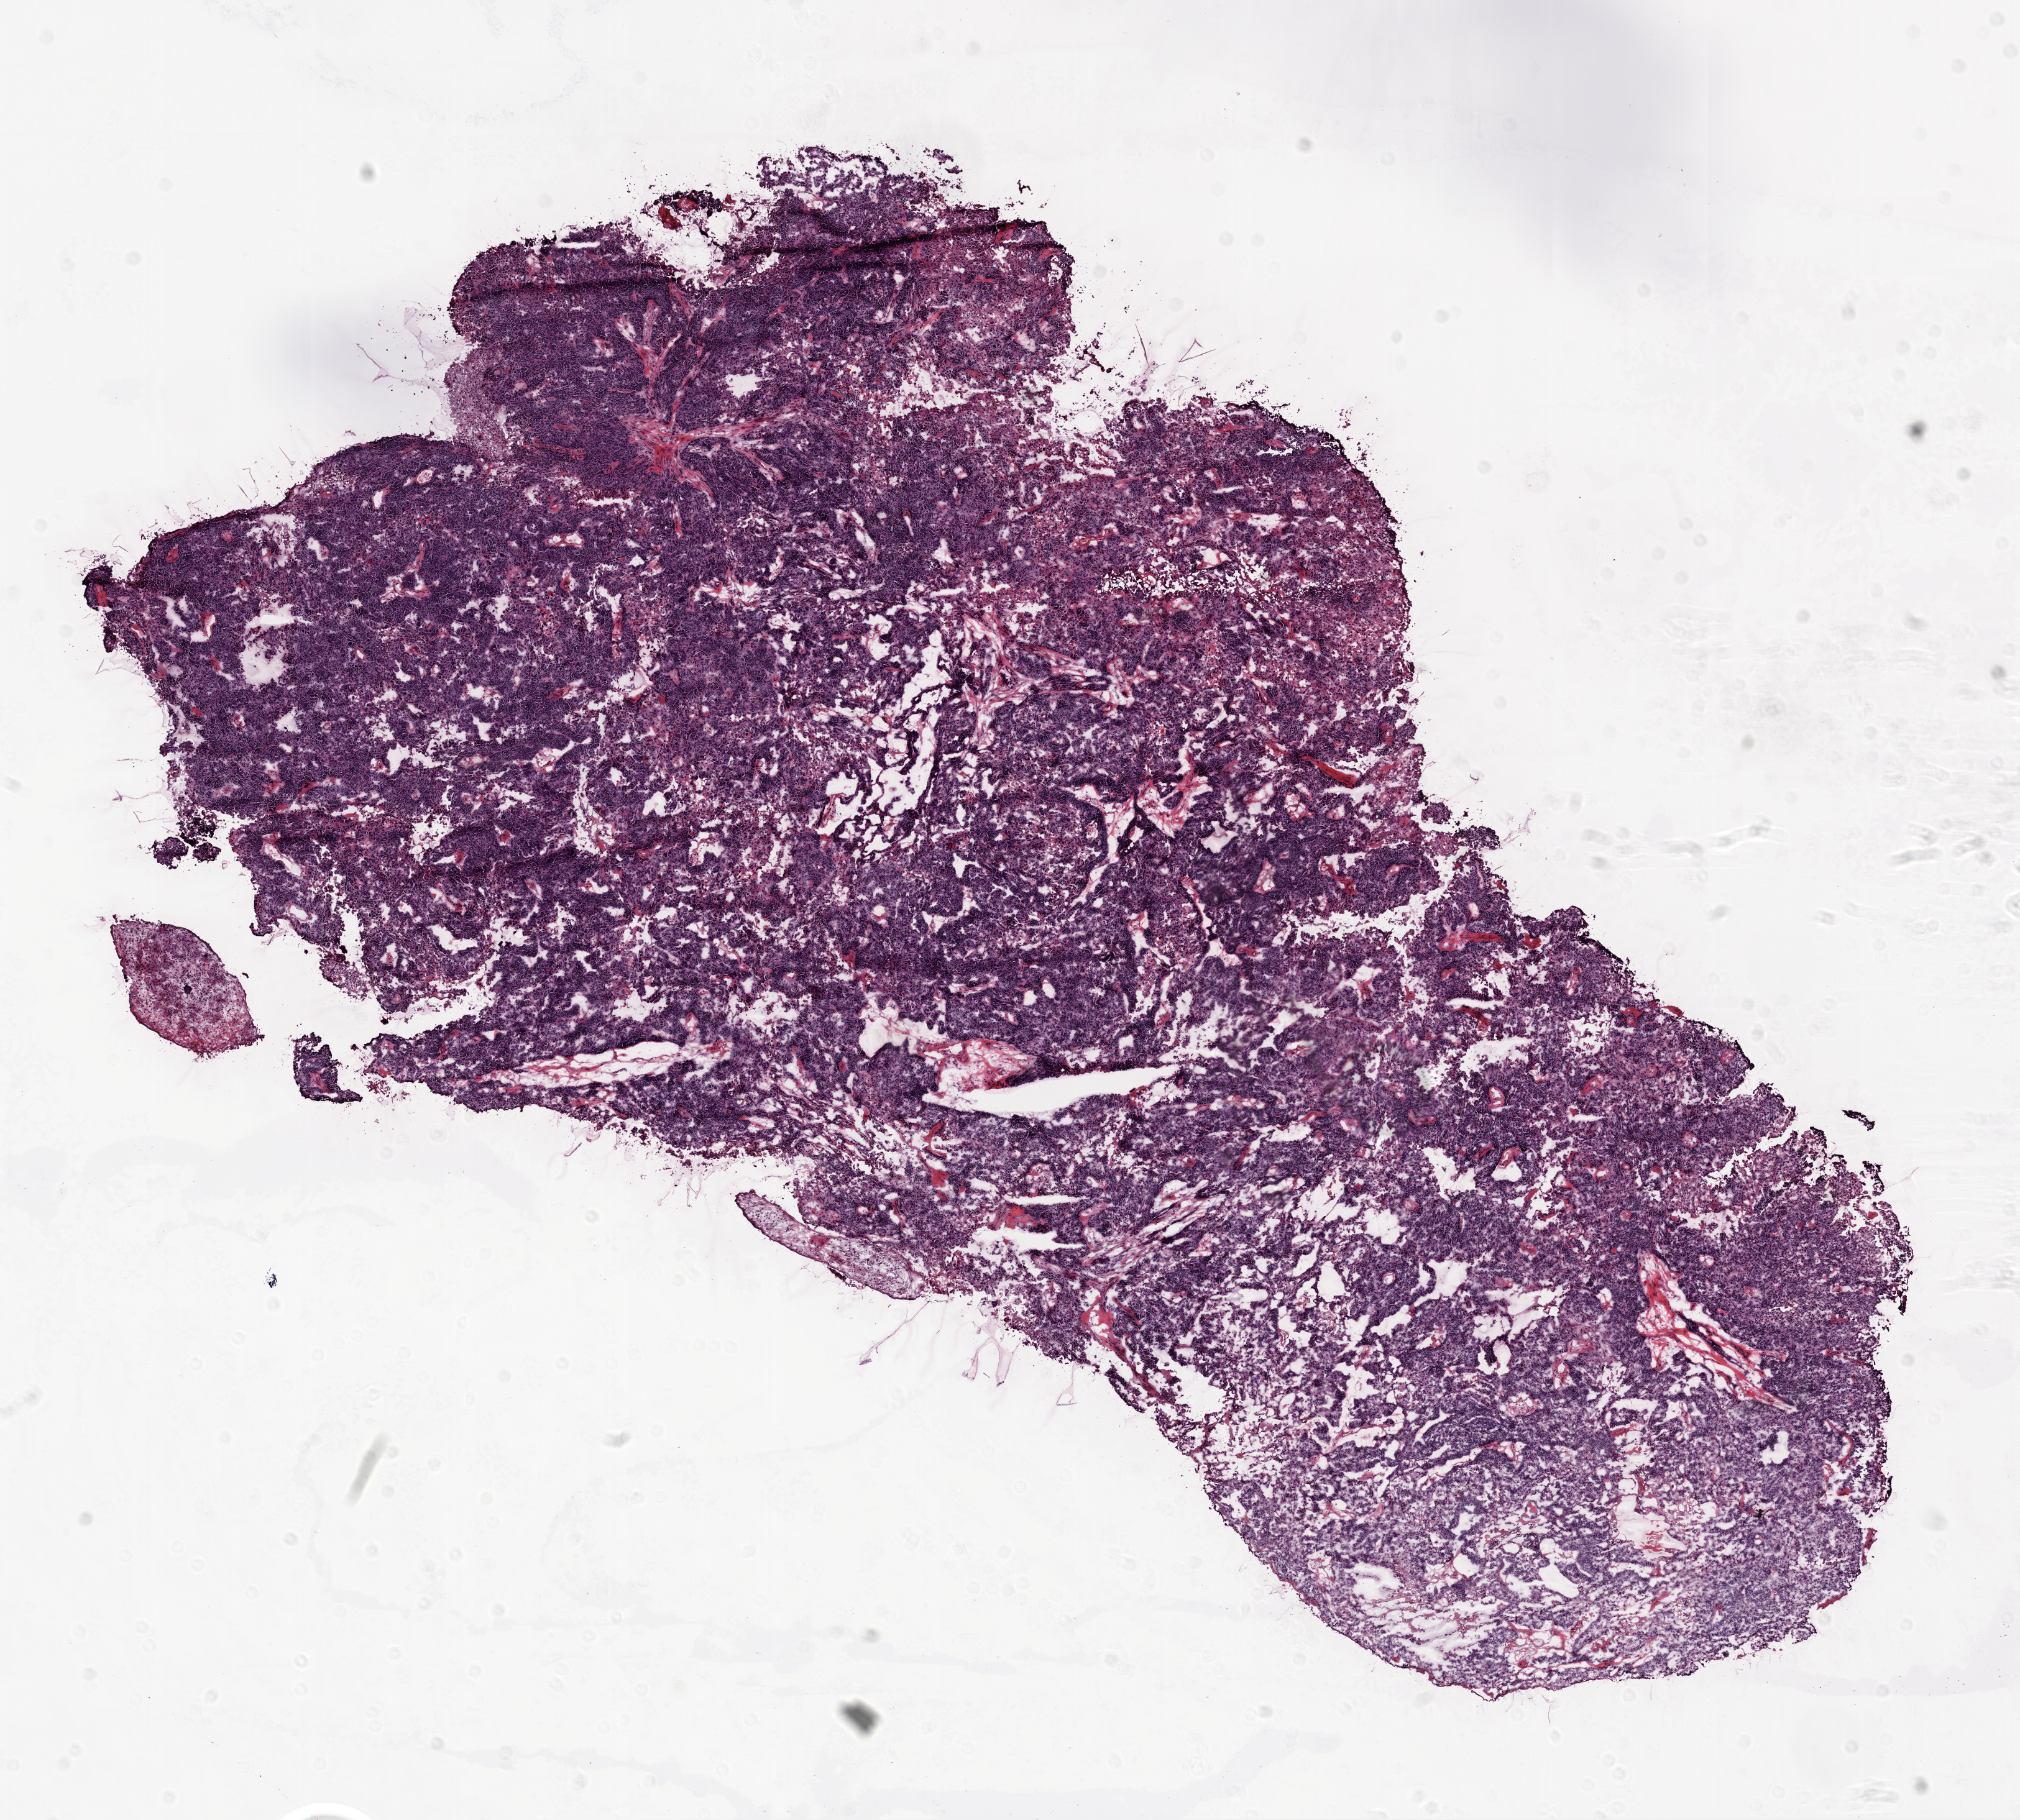
Hematoxylin and eosin (H&E) stained whole-slide image, a low-resolution overview of the entire scanned area, about 13.0 x 11.8 mm. Frozen section. Primary tumour sample from the ovary. Female, age 84 years at initial diagnosis. Histologic grade: G3 (poorly differentiated). Composition of this section per pathologist review: tumour cells 98%, tumour nuclei 95%, normal cells 0%, stromal cells 0%, necrosis 2%.
Diagnosis: Serous cystadenocarcinoma, NOS. FIGO stage: IIIC.